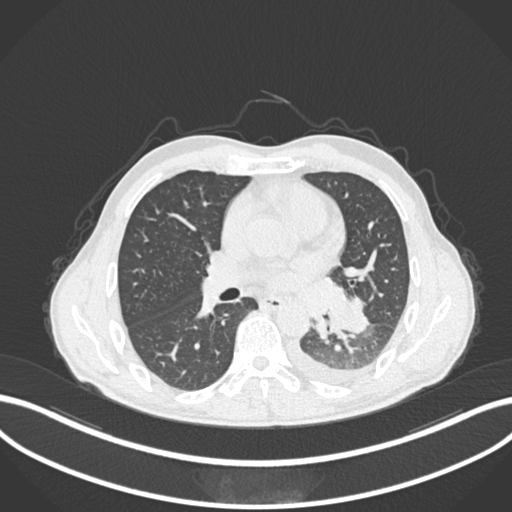
Chest CT, one axial slice; position 126 of 222 along the scan axis; reconstruction kernel B30f; 120 kVp; lung window (W 1500 / L -600 HU); 1 mm slice thickness; 512 × 512 image matrix. Patient: male, 47 years. From the clinical record (not read from this slice): clinical TNM (as recorded): T3 N1 M1c.
Structures marked on this image (bounding box drawn by a radiologist):
- lung tumour (recorded histology: small cell carcinoma): bounding box (x1, y1, x2, y2) in pixels: (326, 286, 374, 337)